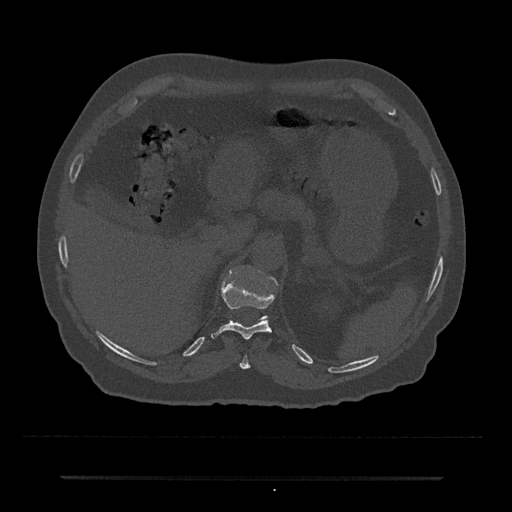
CT including the spine, one axial slice. Position 176 of 797 along the scan axis. 120 kVp. Bone window (W 1800 / L 400 HU). 0.5 mm slice thickness. 512 × 512 image matrix, field of view 437 × 437 mm. Male patient, age 69 years. From the clinical record (not read from this slice): primary cancer: prostate.
Annotated regions visible in this slice (semi-automatically segmented with operator editing):
- T10 vertebra: bounding box [x1, y1, x2, y2] px = [240, 356, 251, 369]
- T11 vertebra: [211, 279, 275, 339]
- T12 vertebra: [262, 277, 278, 319]